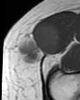
MRI of an extremity soft-tissue mass, one axial slice. Position 17 of 46 along the scan axis. MR volume resampled by the dataset authors to the PET/CT grid (not the native acquisition matrix). 3.27 mm slice thickness. 80 × 100 image matrix, field of view 78 × 98 mm. Female patient. Case-level facts recorded for this patient, not image findings: histological type: synovial sarcoma; grade: intermediate; site of the primary tumour: right thigh.
Structures marked on this image (expert contour drawn on MRI and transferred to this co-registered scan by the dataset authors):
- gross tumour volume including surrounding oedema: bounding box (x1, y1, x2, y2) in pixels: (16, 24, 61, 63)
- gross tumour volume (mass): (16, 24, 61, 63)